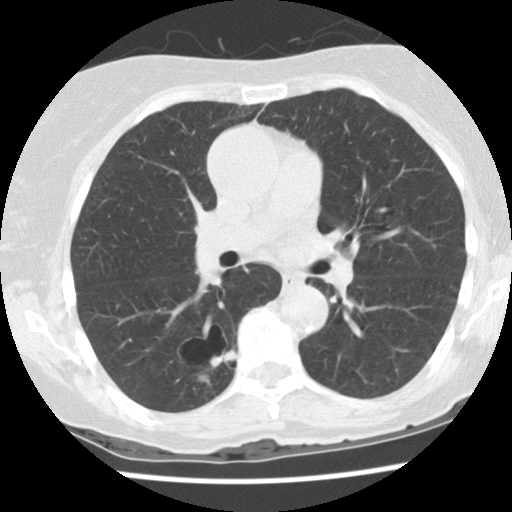
Low-dose screening chest CT, one axial slice. Slice 81 of 136 in the series (ordered by position). Reconstruction kernel STANDARD. 120 kVp. Lung window (W 1500 / L -600 HU). 2.5 mm slice thickness. 512 × 512 image matrix, field of view 300 × 300 mm.
Annotated regions visible in this slice (expert manual segmentation):
- lesion 1 (tumor, lower lobe of right lung): box from (x=209, y=351) to (x=236, y=369) px